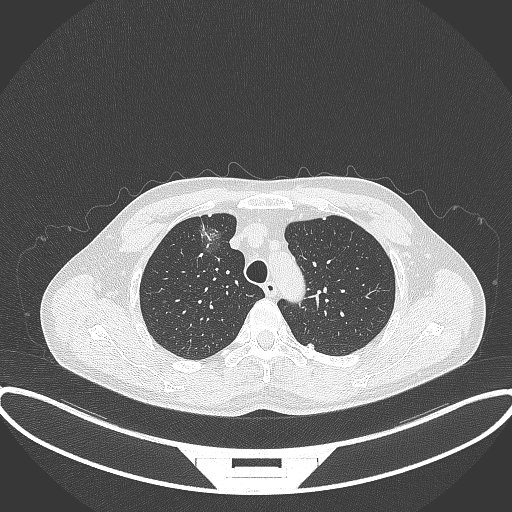
Chest CT, one axial slice; position 285 of 395 along the scan axis; 120 kVp; lung window (W 1500 / L -600 HU); 512 × 512 image matrix, field of view 424 × 424 mm. Patient: male, 60 years. Case-level facts recorded for this patient, not image findings: clinical TNM (as recorded): T1c N0 M0.
Structures marked on this image (bounding box drawn by a radiologist):
- lung tumour (recorded histology: adenocarcinoma): box from (x=198, y=212) to (x=230, y=260) px